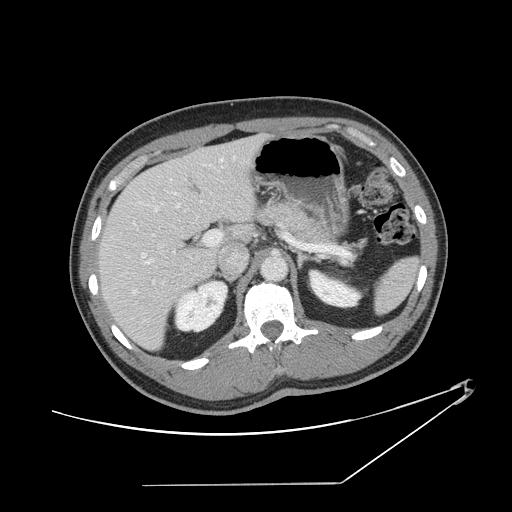
Contrast-enhanced abdominal CT, one axial slice; position 85 of 152 along the scan axis; reconstruction kernel STANDARD; 120 kVp; intravenous contrast given; soft-tissue window (W 400 / L 40 HU); 2.5 mm slice thickness; 512 × 512 image matrix, field of view 432 × 432 mm. Male patient, age 45 years. Case-level facts recorded for this patient, not image findings: diagnosis: colorectal cancer liver metastases, imaged before liver resection.
Structures marked on this image (outlined manually by an expert reader):
- hepatic veins: bounding box [x1, y1, x2, y2] px = [112, 157, 224, 294]
- liver: [100, 136, 262, 349]
- planned liver remnant (the part of the liver to remain after resection): [100, 156, 223, 349]
- portal vein (with intrahepatic branches): [145, 193, 314, 264]